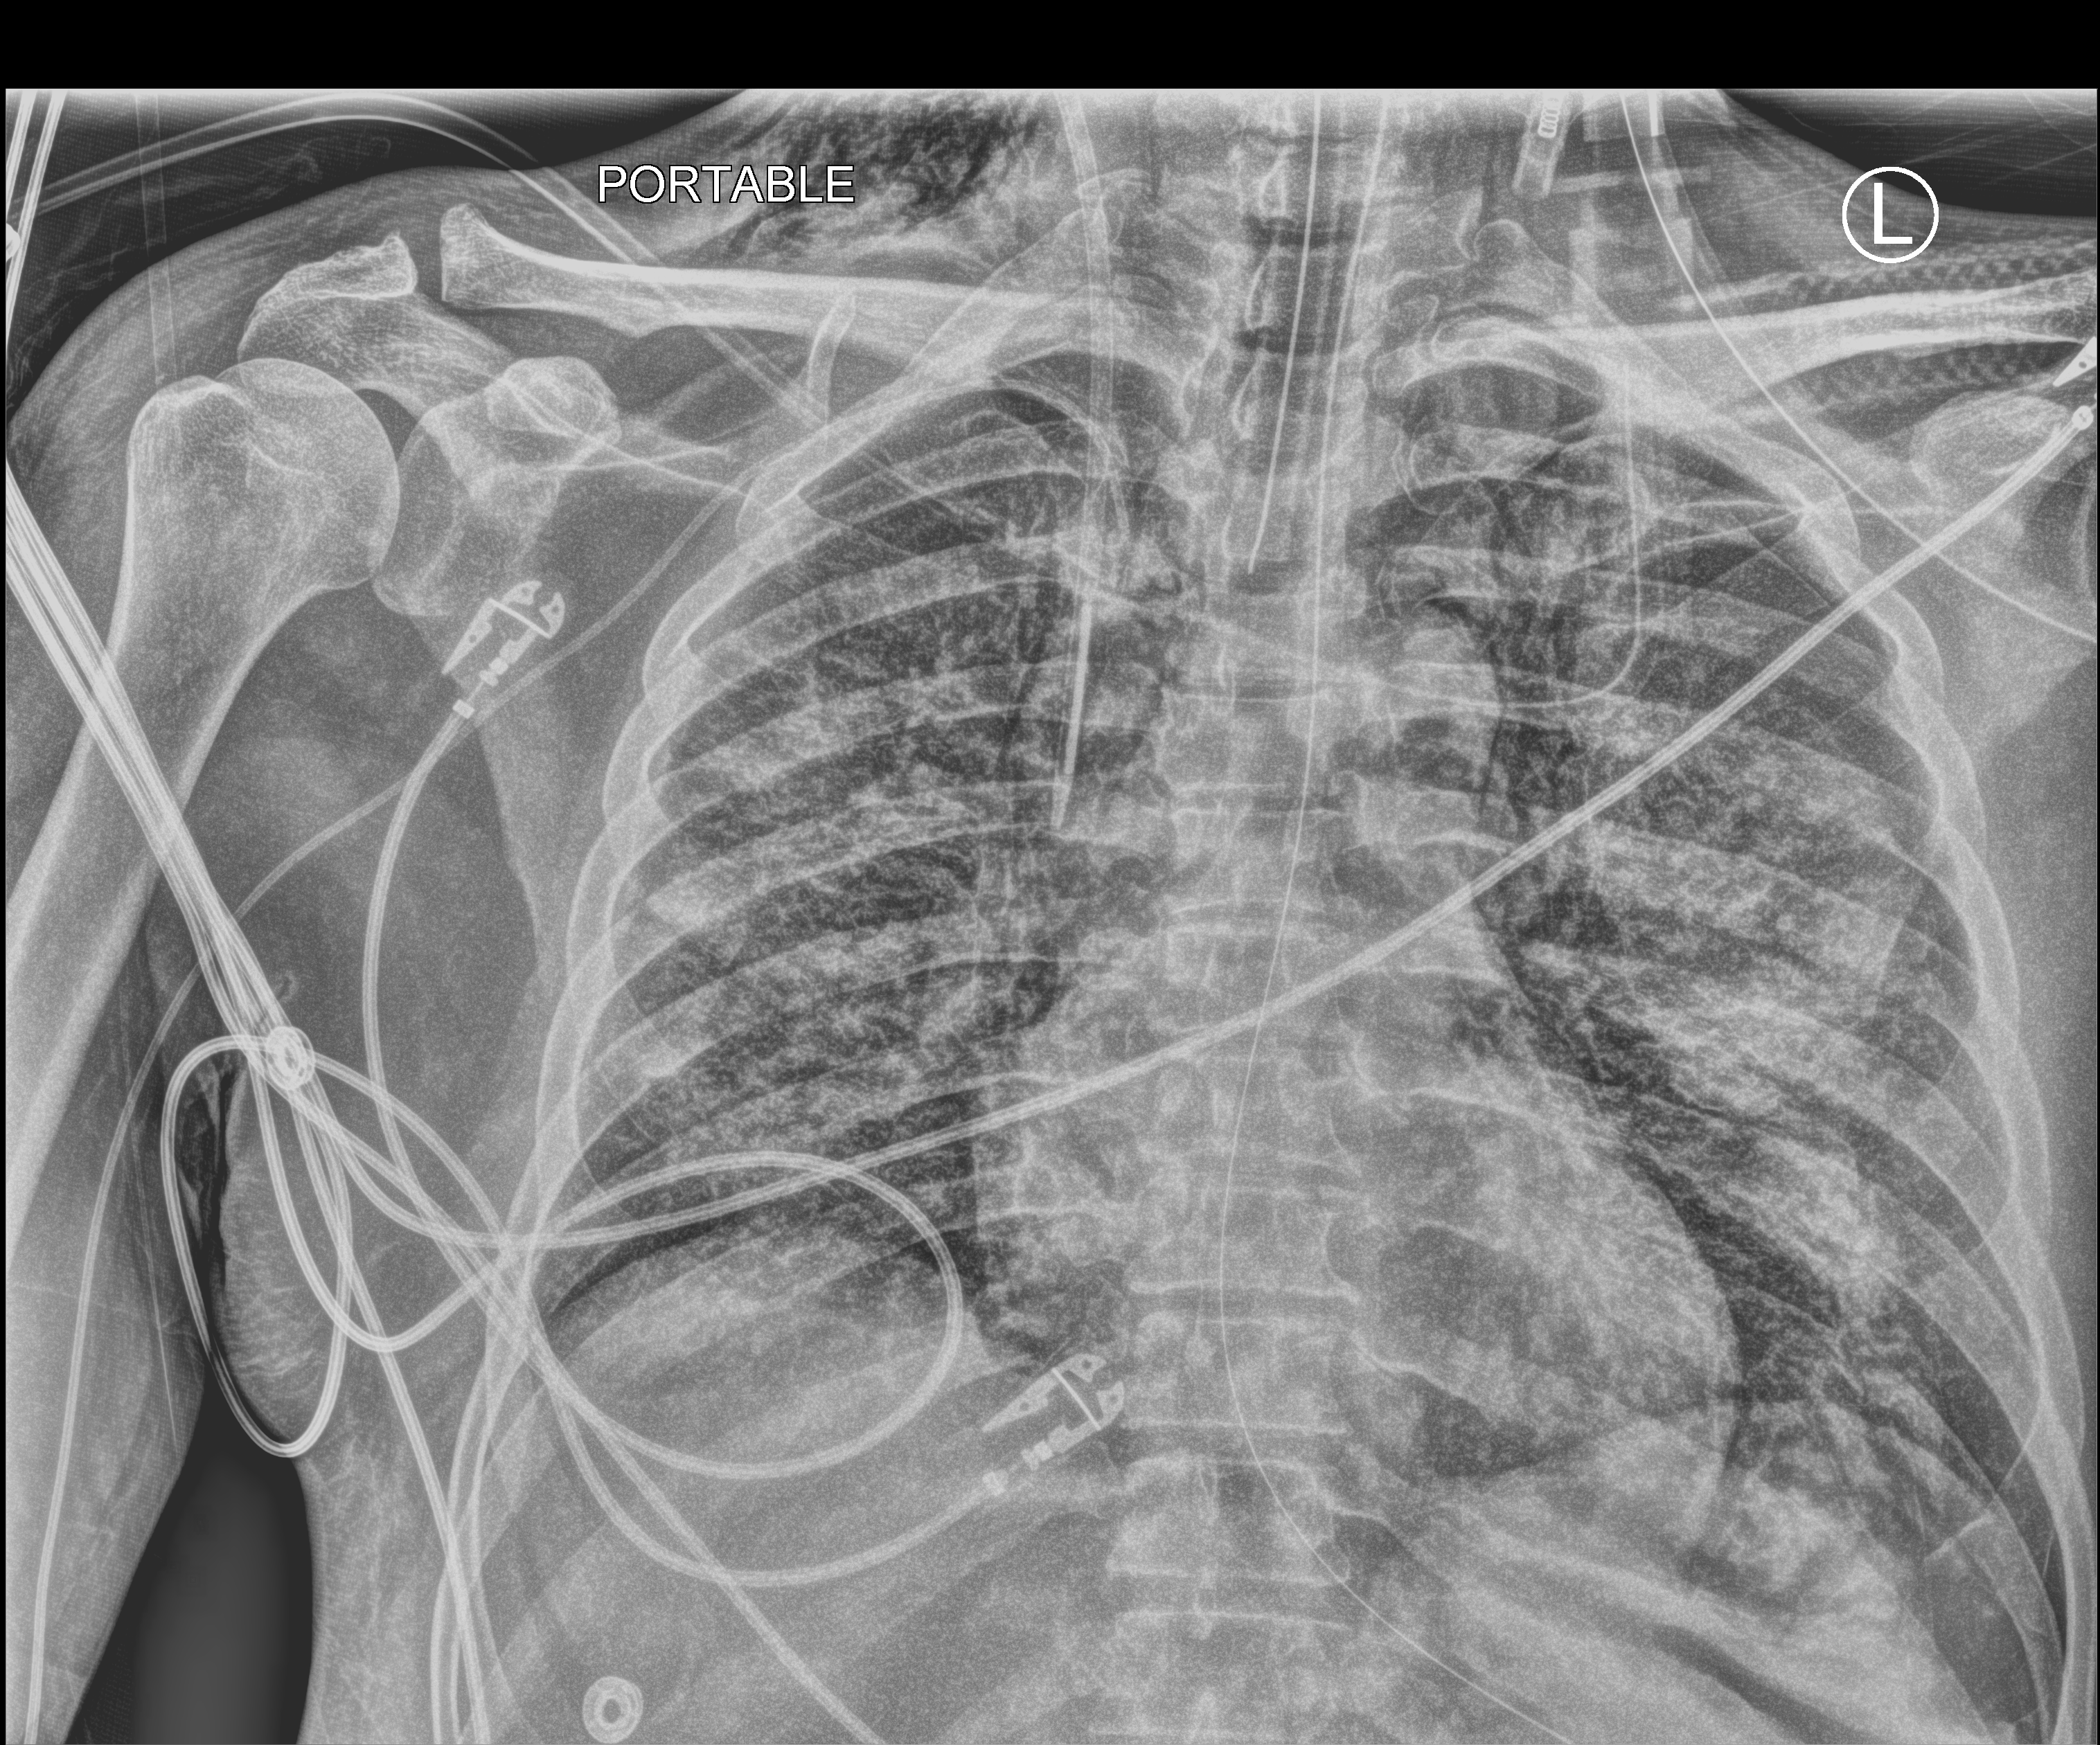
Chest X-ray (portable); anteroposterior (AP) projection. Patient hospitalised with COVID-19; male, aged 18–59 years.
From the hospital-stay record, not from the radiograph (when in the stay this image was taken is not recorded): admitted to intensive care during this hospital stay: yes; smoking status (admission record): never.